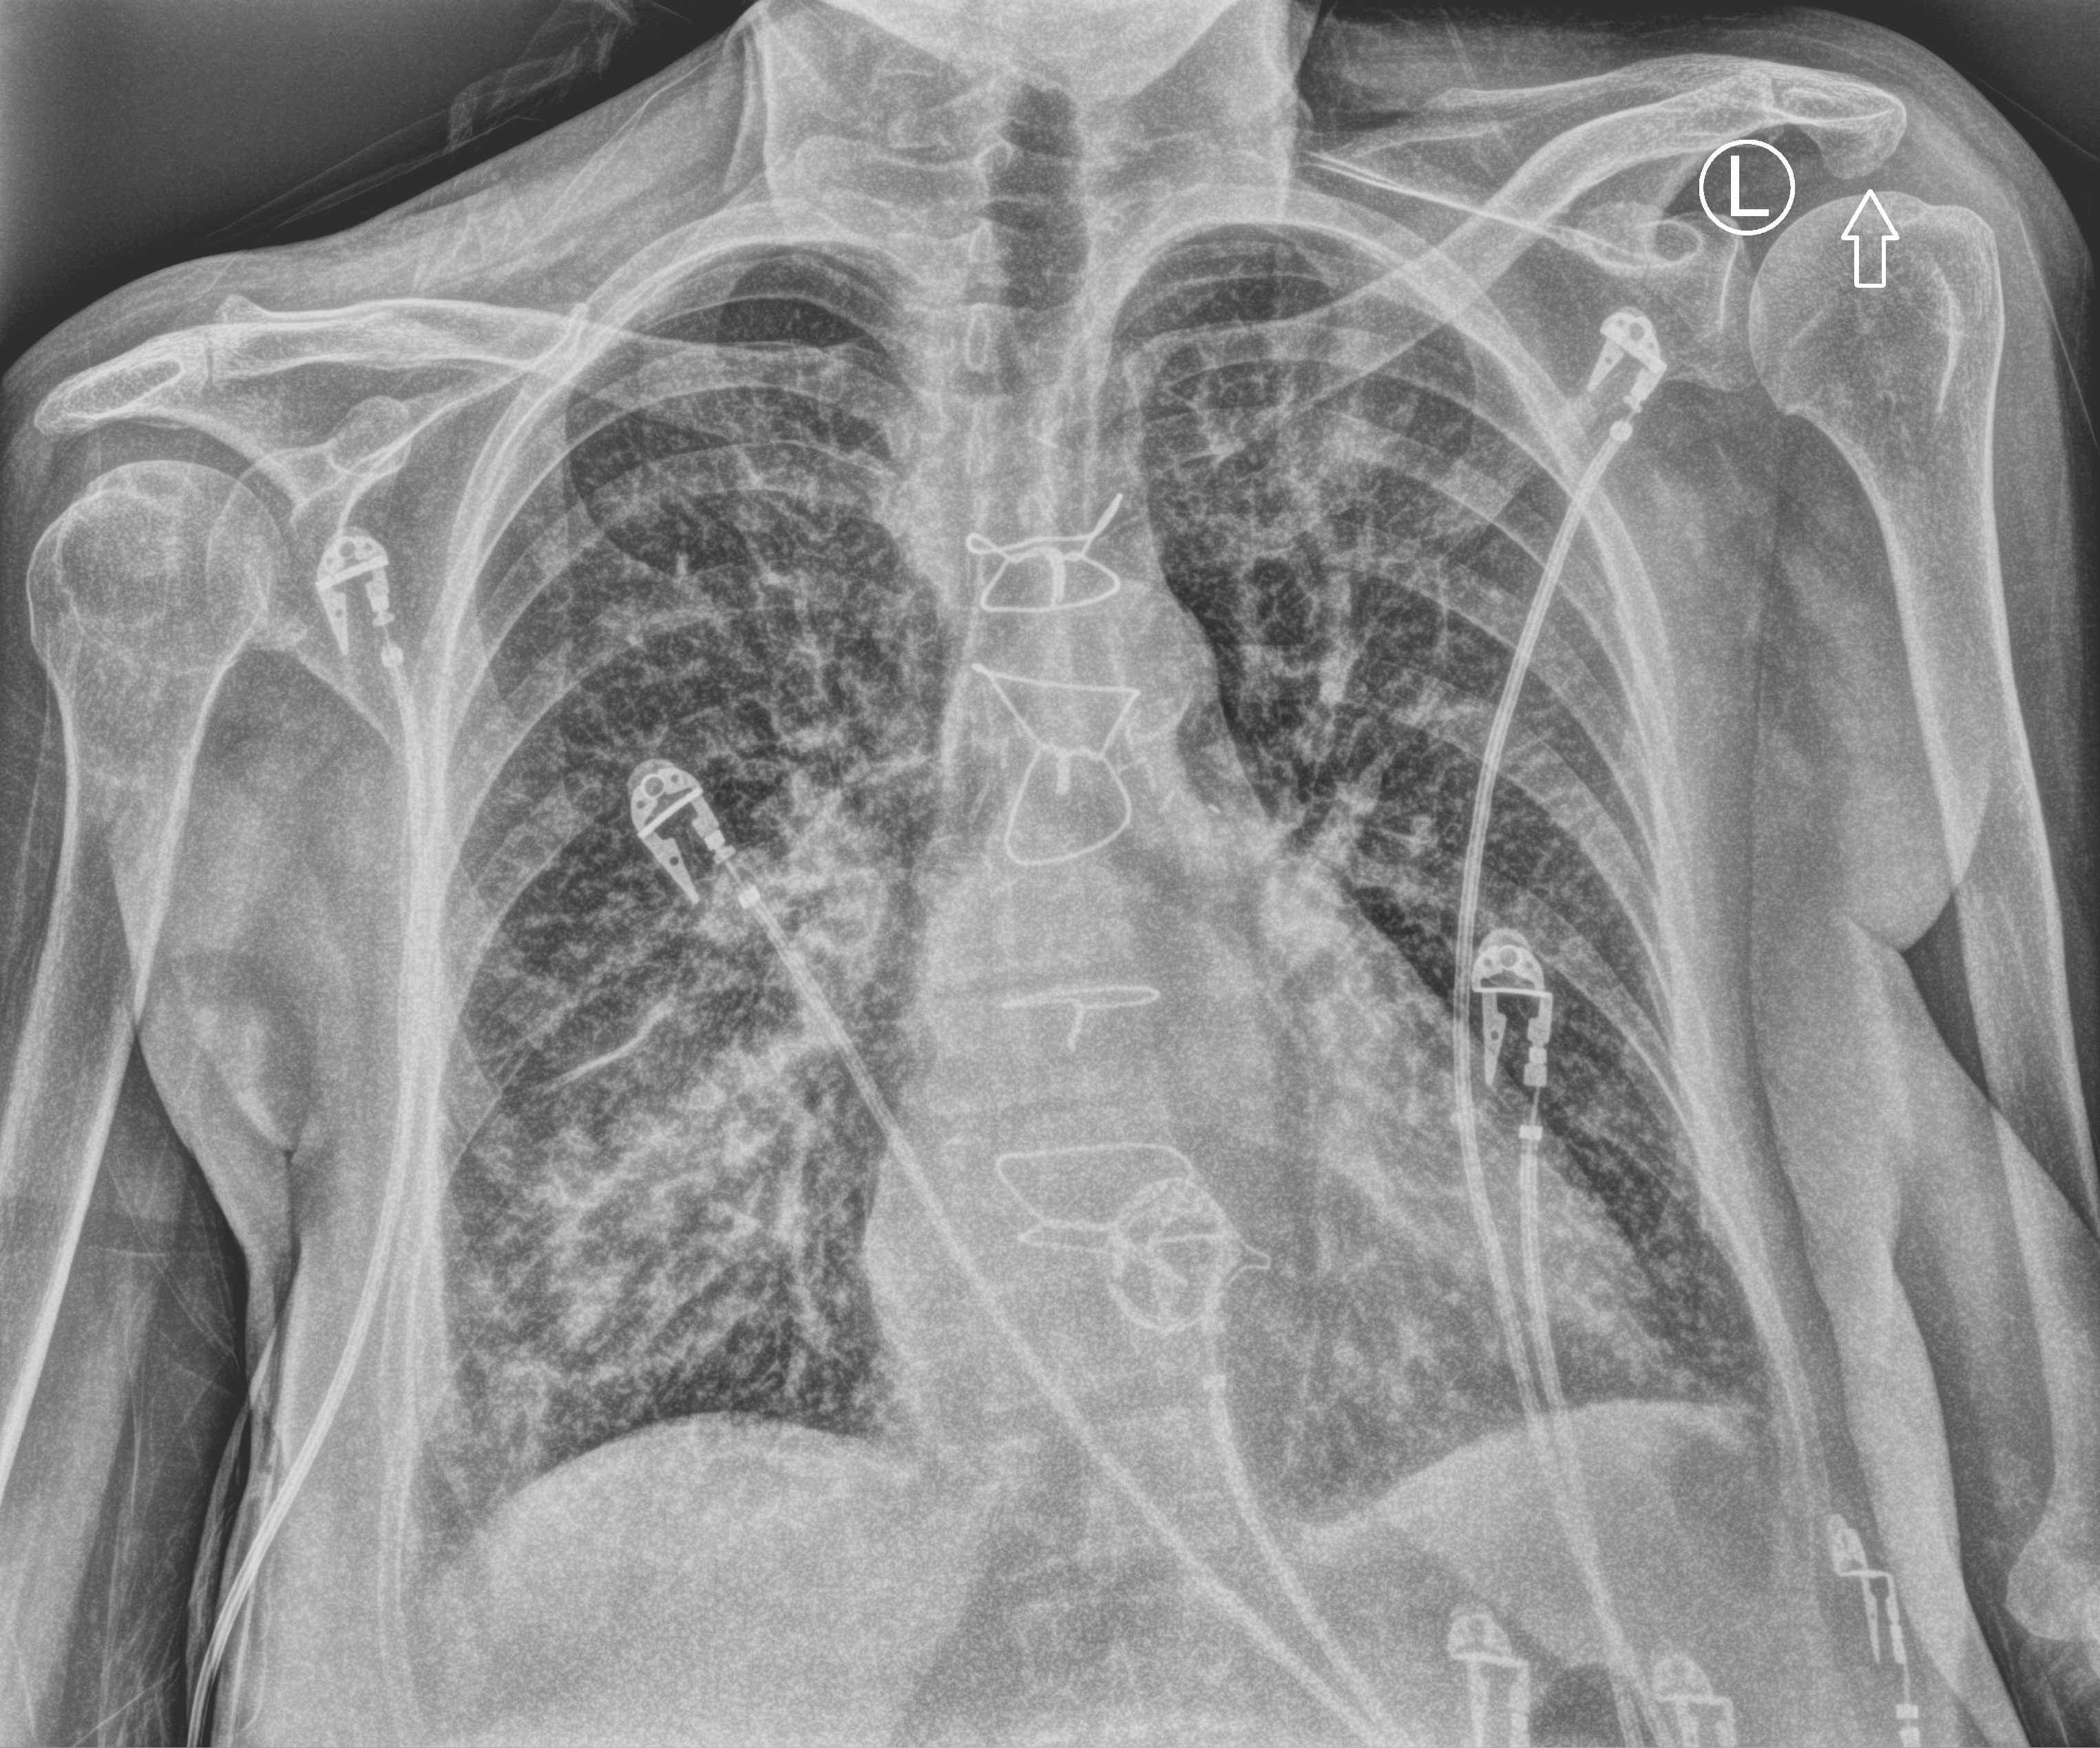
Portable chest radiograph. Female patient hospitalised with COVID-19, age 60–74 years.
From the hospital-stay record, not from the radiograph (when in the stay this image was taken is not recorded): admitted to intensive care during this hospital stay: yes.